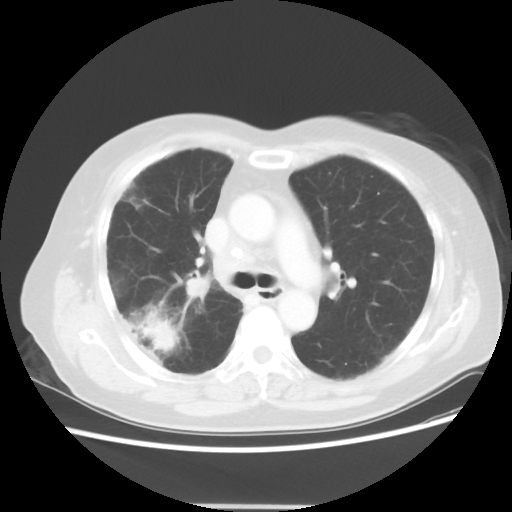
Chest CT, one axial slice. Position 31 of 50 along the scan axis. Reconstruction kernel STANDARD. Lung window (W 1500 / L -600 HU). 512 × 512 image matrix. Patient: female, 72 years. From the clinical record (not read from this slice): clinical TNM (as recorded): T2 N1 M0.
Outlined on this slice (bounding box drawn by a radiologist):
- lung tumour (recorded histology: adenocarcinoma): bounding box [x1, y1, x2, y2] px = [136, 312, 177, 353]